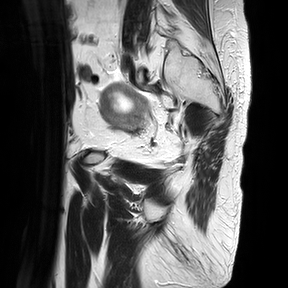
Pelvic MRI for cervical cancer, one sagittal slice. Slice 6 of 30 in the series (ordered by position). T2-weighted. 1.5 T. TE 100 ms, TR 4816.3 ms. 288 × 288 image matrix. Female patient, age 74 years.
Outlined on this slice (outlined manually by an expert reader):
- uterus and cervix: box from (x=99, y=83) to (x=148, y=132) px